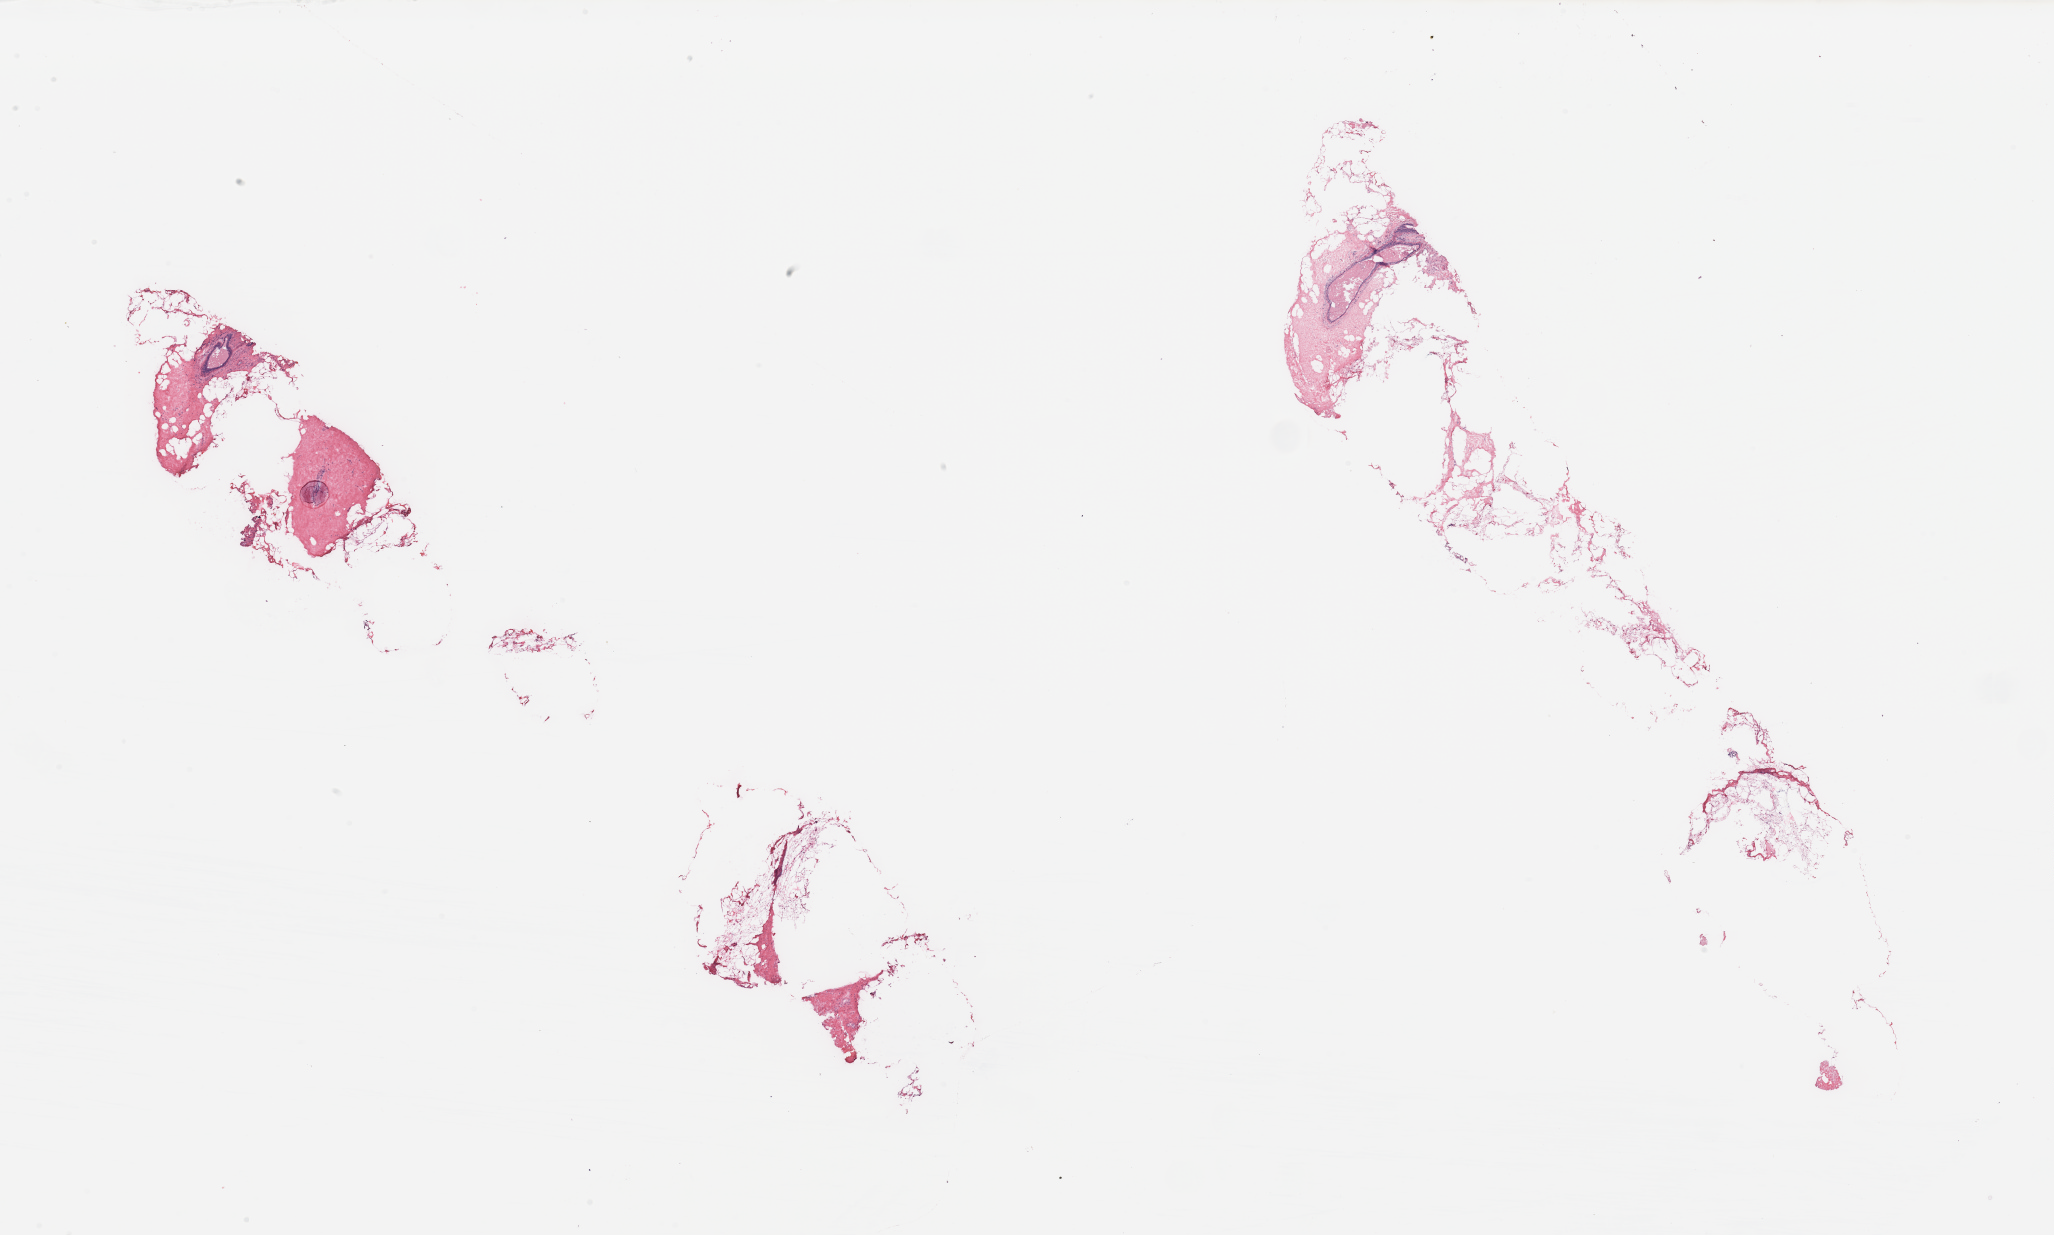
H&E-stained whole-slide image — low-resolution overview of the scanned area, about 32.5 x 19.5 mm; breast, tissue type not recorded.
* patient diagnosis (cohort enrolment): breast cancer (breast)